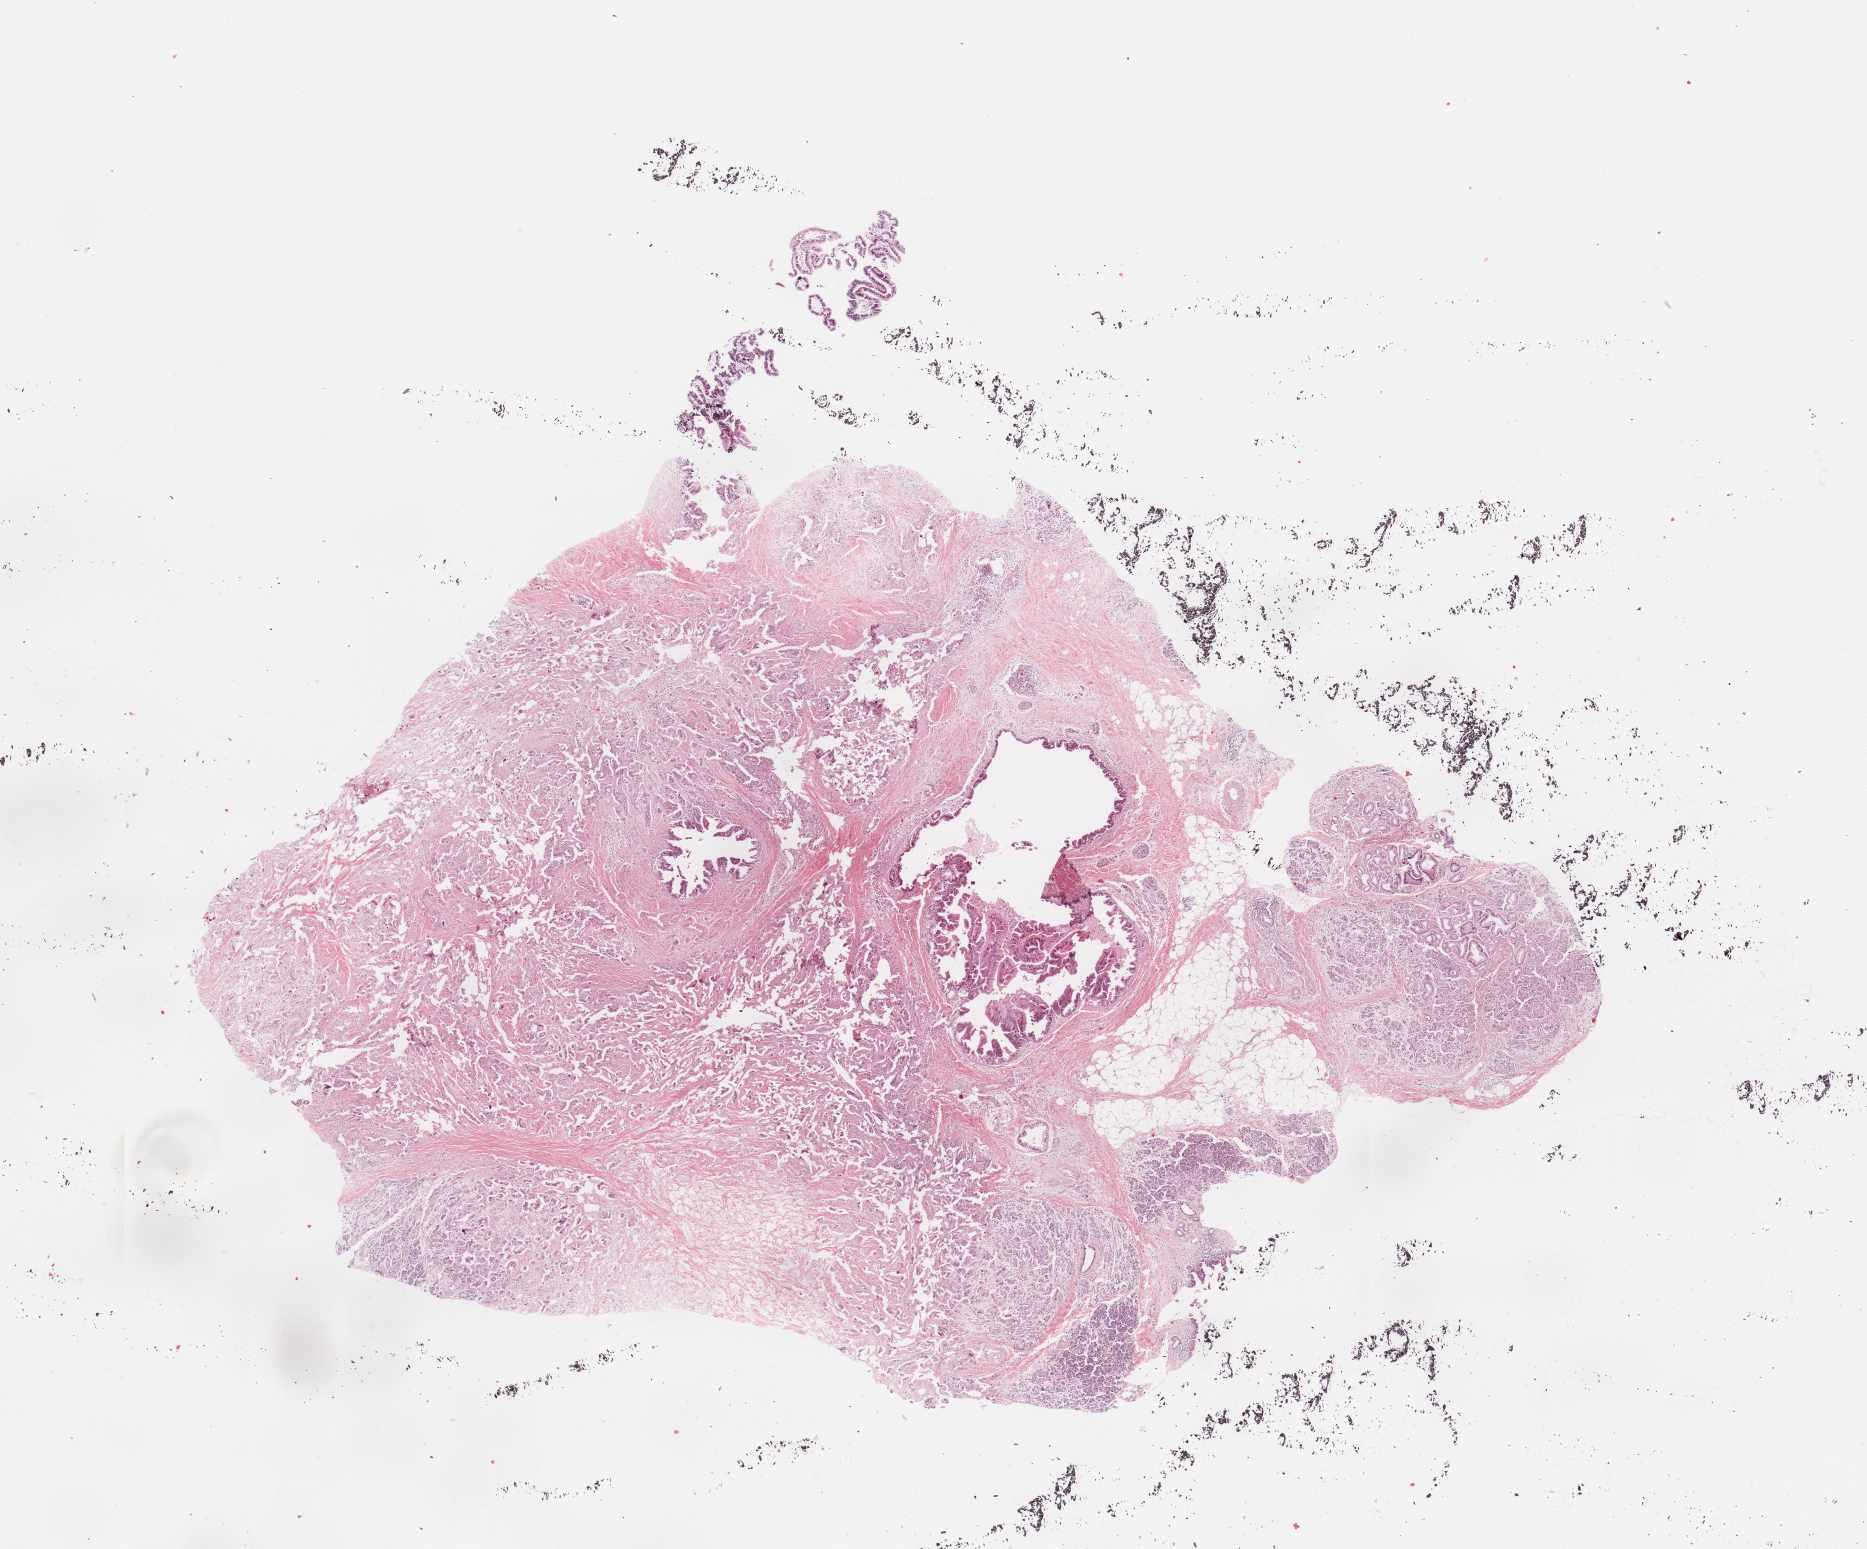
Whole-slide histology image, H&E-stained — a low-resolution overview of the entire scanned area, about 14.8 x 12.3 mm. Tumour tissue sample, sampled site: pancreas. Patient: male, age 64 years. Histologic grade: G2 (moderately differentiated). Composition of this section per pathologist review: tumour nuclei 60%, necrosis 5%.
Histologic diagnosis: Infiltrating duct carcinoma, NOS. Primary tumour site (as recorded): head. AJCC pathologic stage: III.